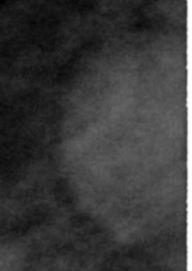
Crop from a digitized film mammogram around one marked abnormality, left breast, CC view.
Mass, shape round, margins circumscribed; BI-RADS assessment category 3; subtlety rating 4 on a 1 (subtle) to 5 (obvious) scale; pathology (as recorded): benign.